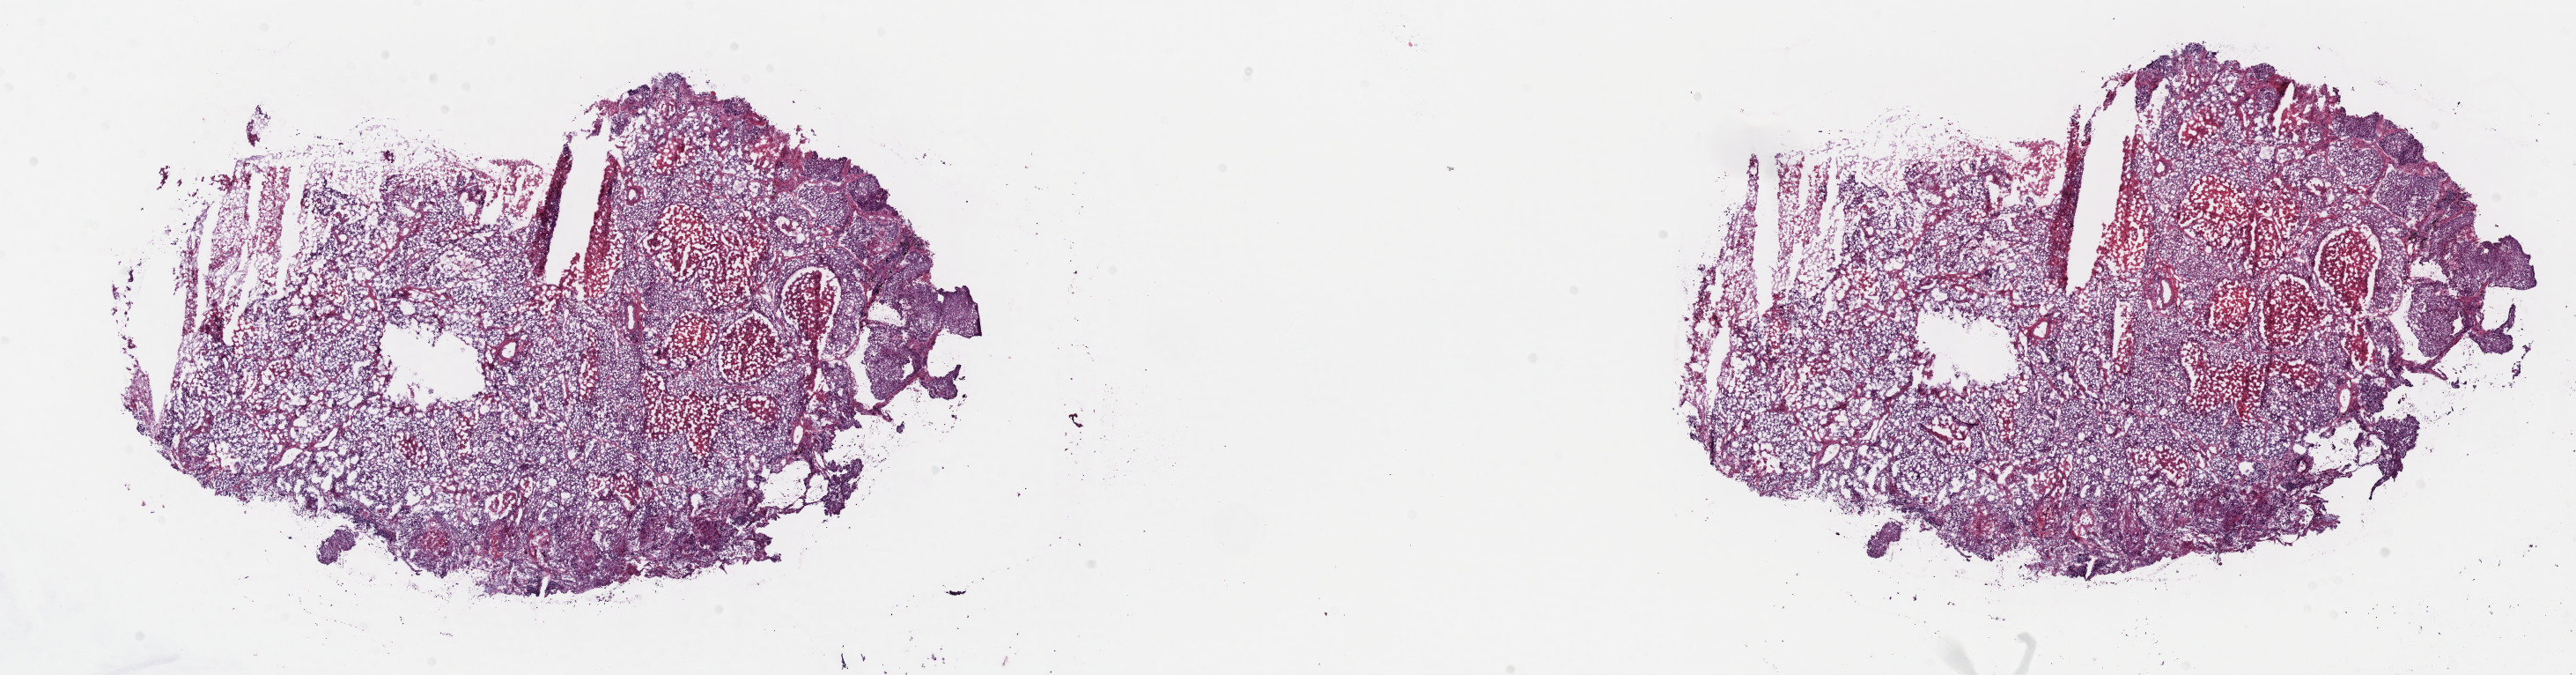
Whole-slide histology image, H&E — whole scanned area (about 23.7 x 6.2 mm, acquisition: 40x scan) shown as a low-resolution overview. Frozen section. Primary tumour sample from the lung. Female patient; age at initial diagnosis 59 years. Composition of this section per pathologist review: tumour cells 75%, tumour nuclei 75%, normal cells 5%, stromal cells 10%, necrosis 10%. Infiltration values recorded for this section: lymphocyte infiltration 2%, monocyte infiltration 2%, neutrophil infiltration 0%.
AJCC pathologic stage: IA (5th edition). Histologic diagnosis: Squamous cell carcinoma, NOS (upper lobe, lung). Laterality: right.